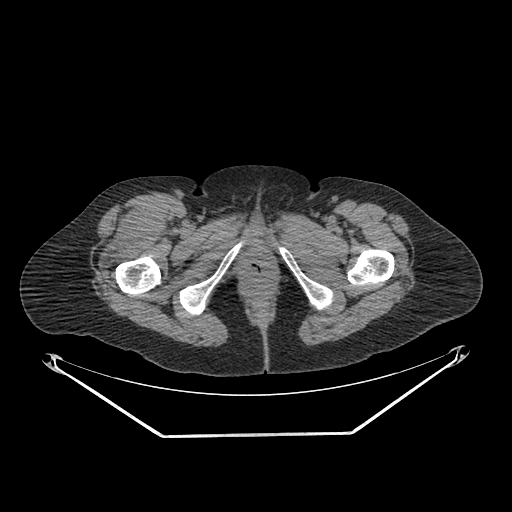
CT of an extremity soft-tissue mass (from a PET/CT study), one axial slice; reconstruction kernel SOFT; 140 kVp; soft-tissue window (W 400 / L 40 HU); 3.75 mm slice thickness; 512 × 512 image matrix, field of view 500 × 500 mm. Female patient. From the clinical record (not read from this slice): histological type: pleiomorphic undifferentiated sarcoma; grade: high; site of the primary tumour: right quadricep.
Structures marked on this image (expert contour drawn on MRI and transferred to this co-registered scan by the dataset authors):
- tumour plus oedema (research contour): bounding box [x1, y1, x2, y2] px = [101, 203, 168, 273]
- tumour (research contour): [114, 203, 168, 250]